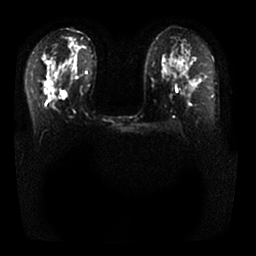
Breast MRI, one axial slice; position 15 of 25 along the scan axis; diffusion-weighted series; image 2 of 4 stored at this slice position (different b-values; order by instance number); 1.5 T; 4 mm slice thickness; 256 × 256 image matrix, field of view 350 × 350 mm. Female patient.
Structures marked on this image (expert manual segmentation):
- tumour on diffusion-weighted imaging: bounding box [x1, y1, x2, y2] px = [51, 102, 54, 108]